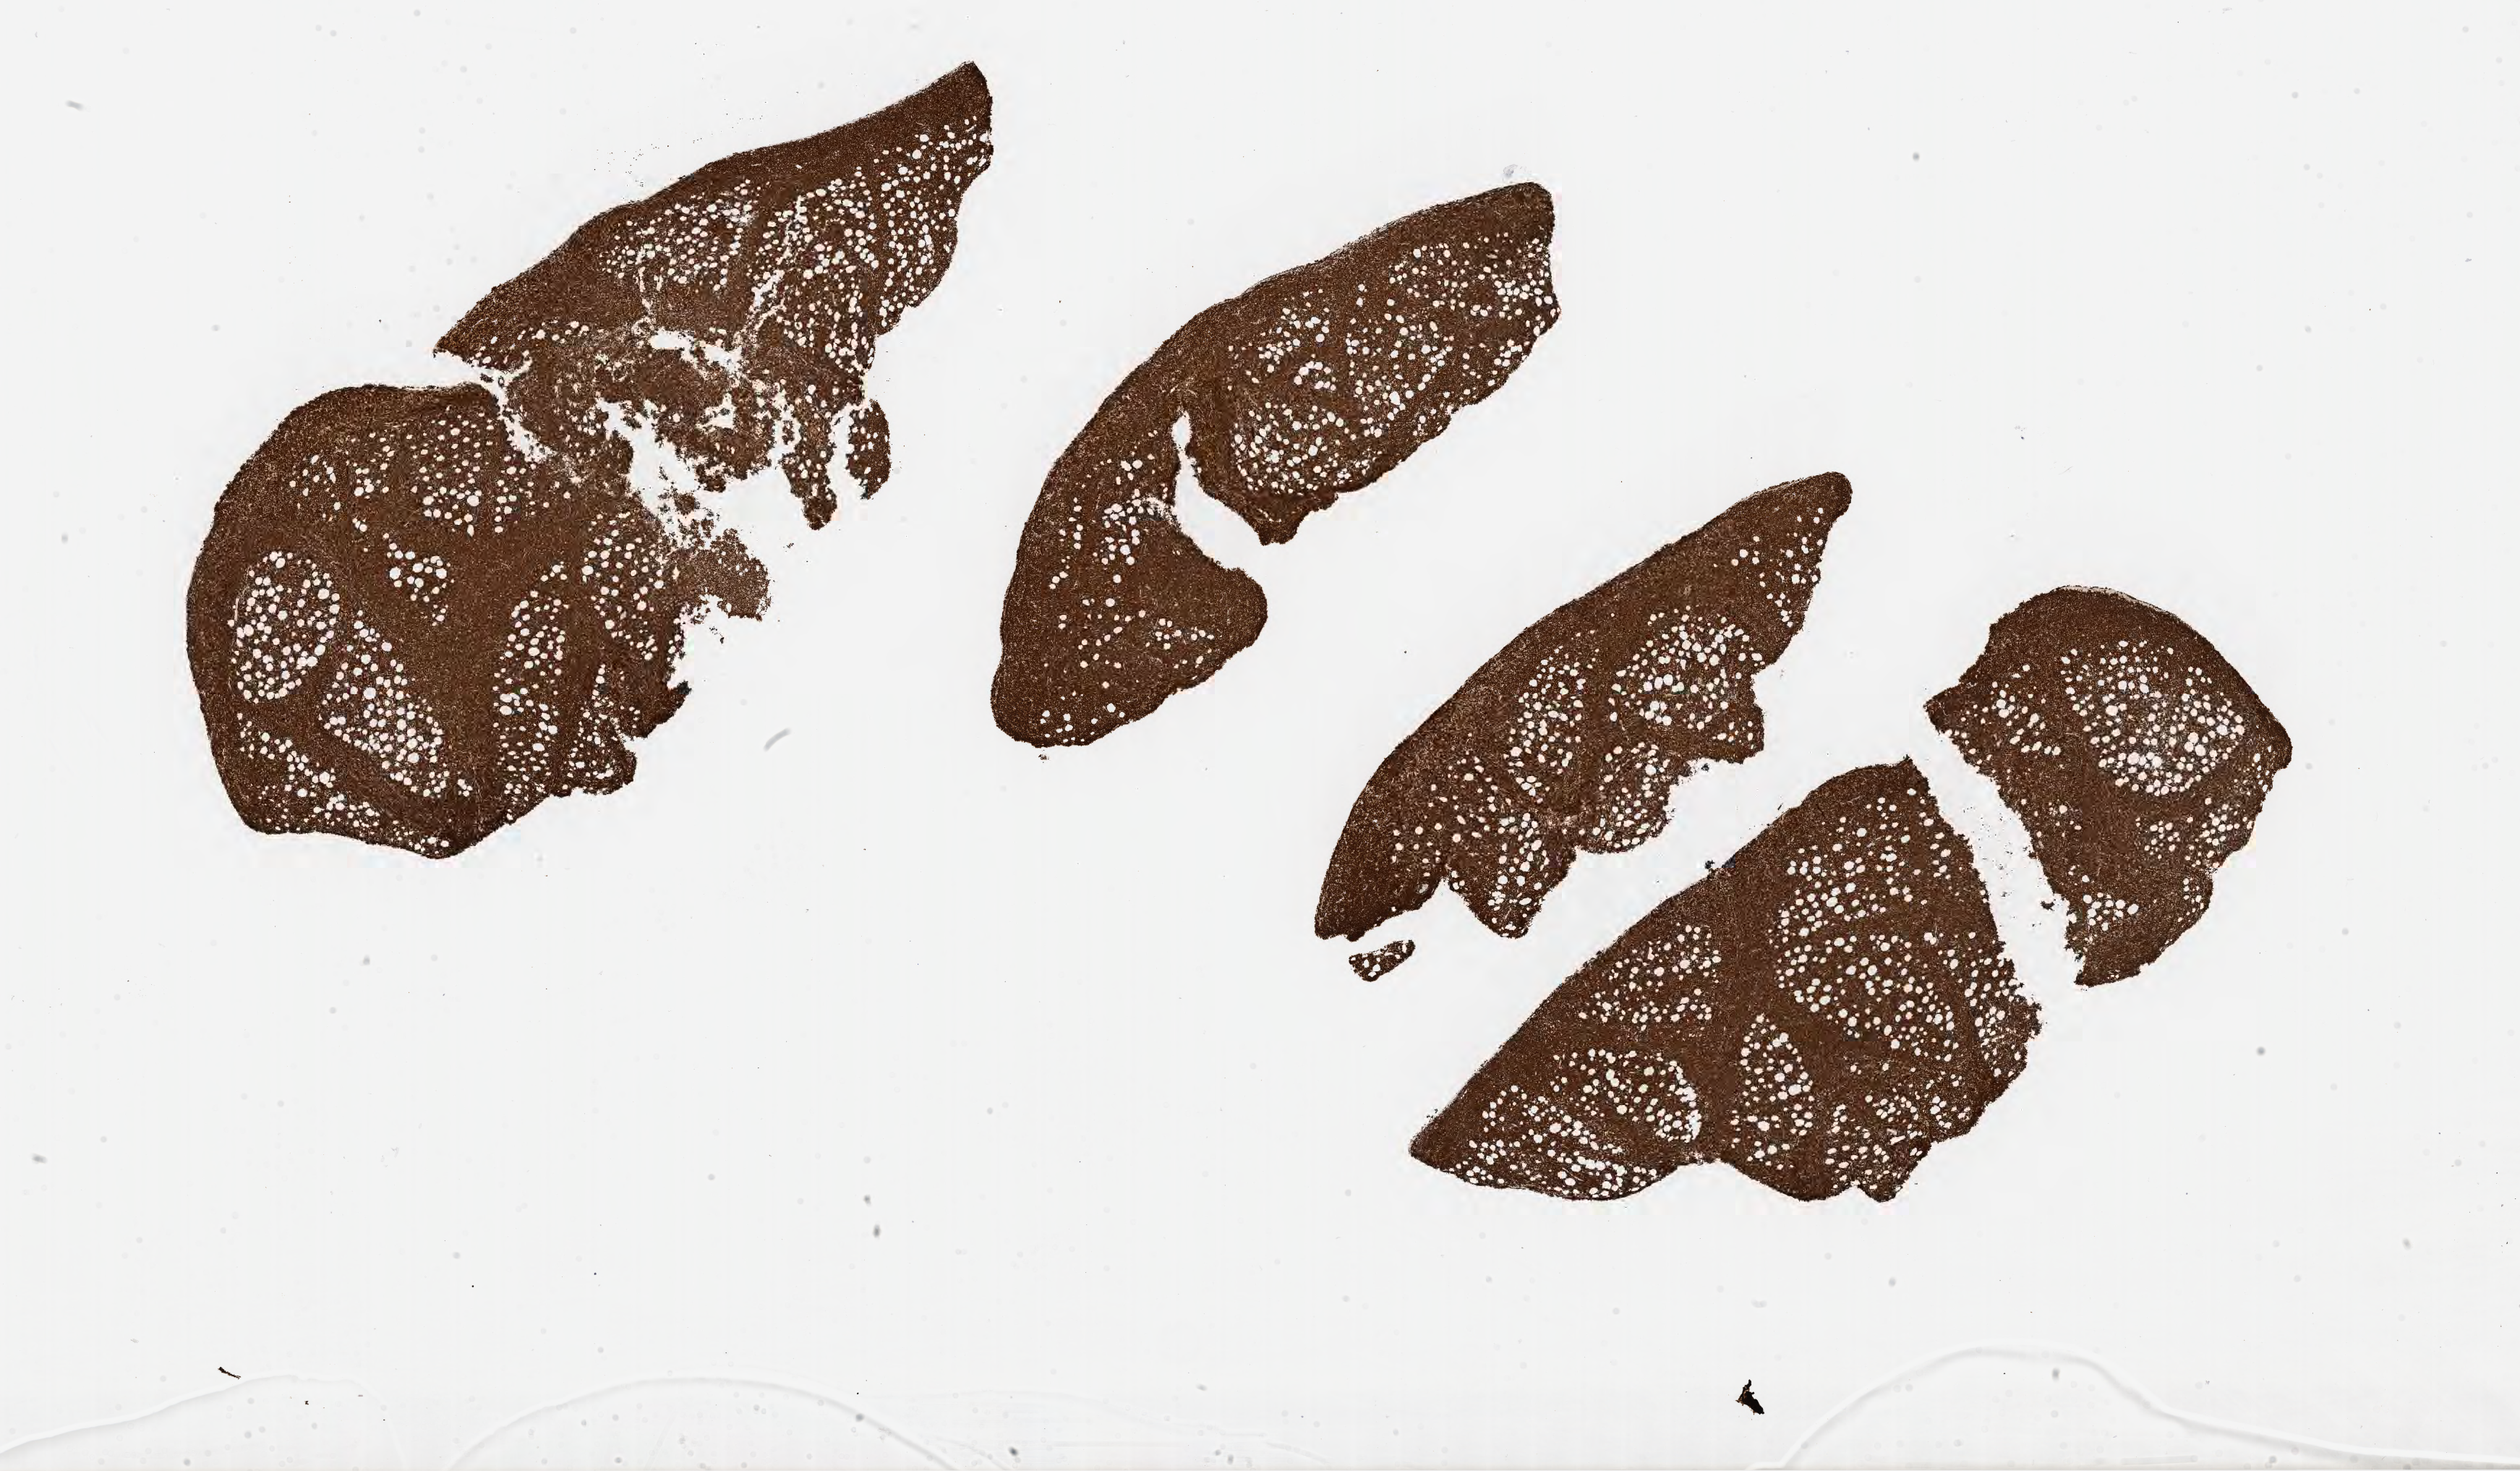
Whole-slide image, immunohistochemical stain for Ki-67, low-resolution overview of the scanned area, about 28.2 x 16.5 mm. Tumor tissue. Patient male; 52 years old.
• histologic diagnosis: Diffuse large B-cell lymphoma, NOS